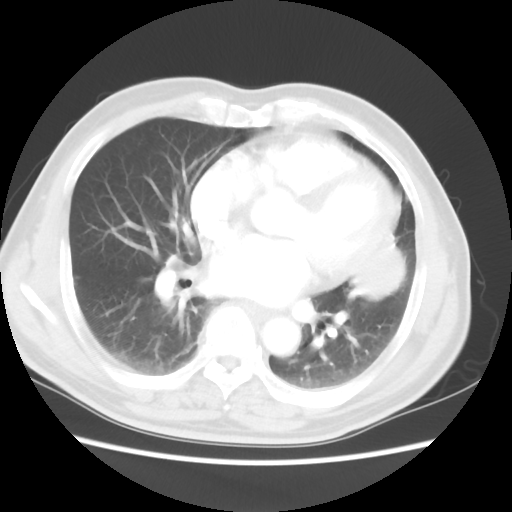
Chest CT, one axial slice. Slice 21 of 50 in the series (ordered by position). Reconstruction kernel STANDARD. 120 kVp. Lung window (W 1500 / L -600 HU). 512 × 512 image matrix. Male patient, age 69 years. Case-level facts recorded for this patient, not image findings: clinical TNM (as recorded): T3 N1 M1a.
Structures marked on this image (bounding box drawn by a radiologist):
- lung tumour (recorded histology: squamous cell carcinoma): bounding box (x1, y1, x2, y2) in pixels: (351, 230, 425, 310)